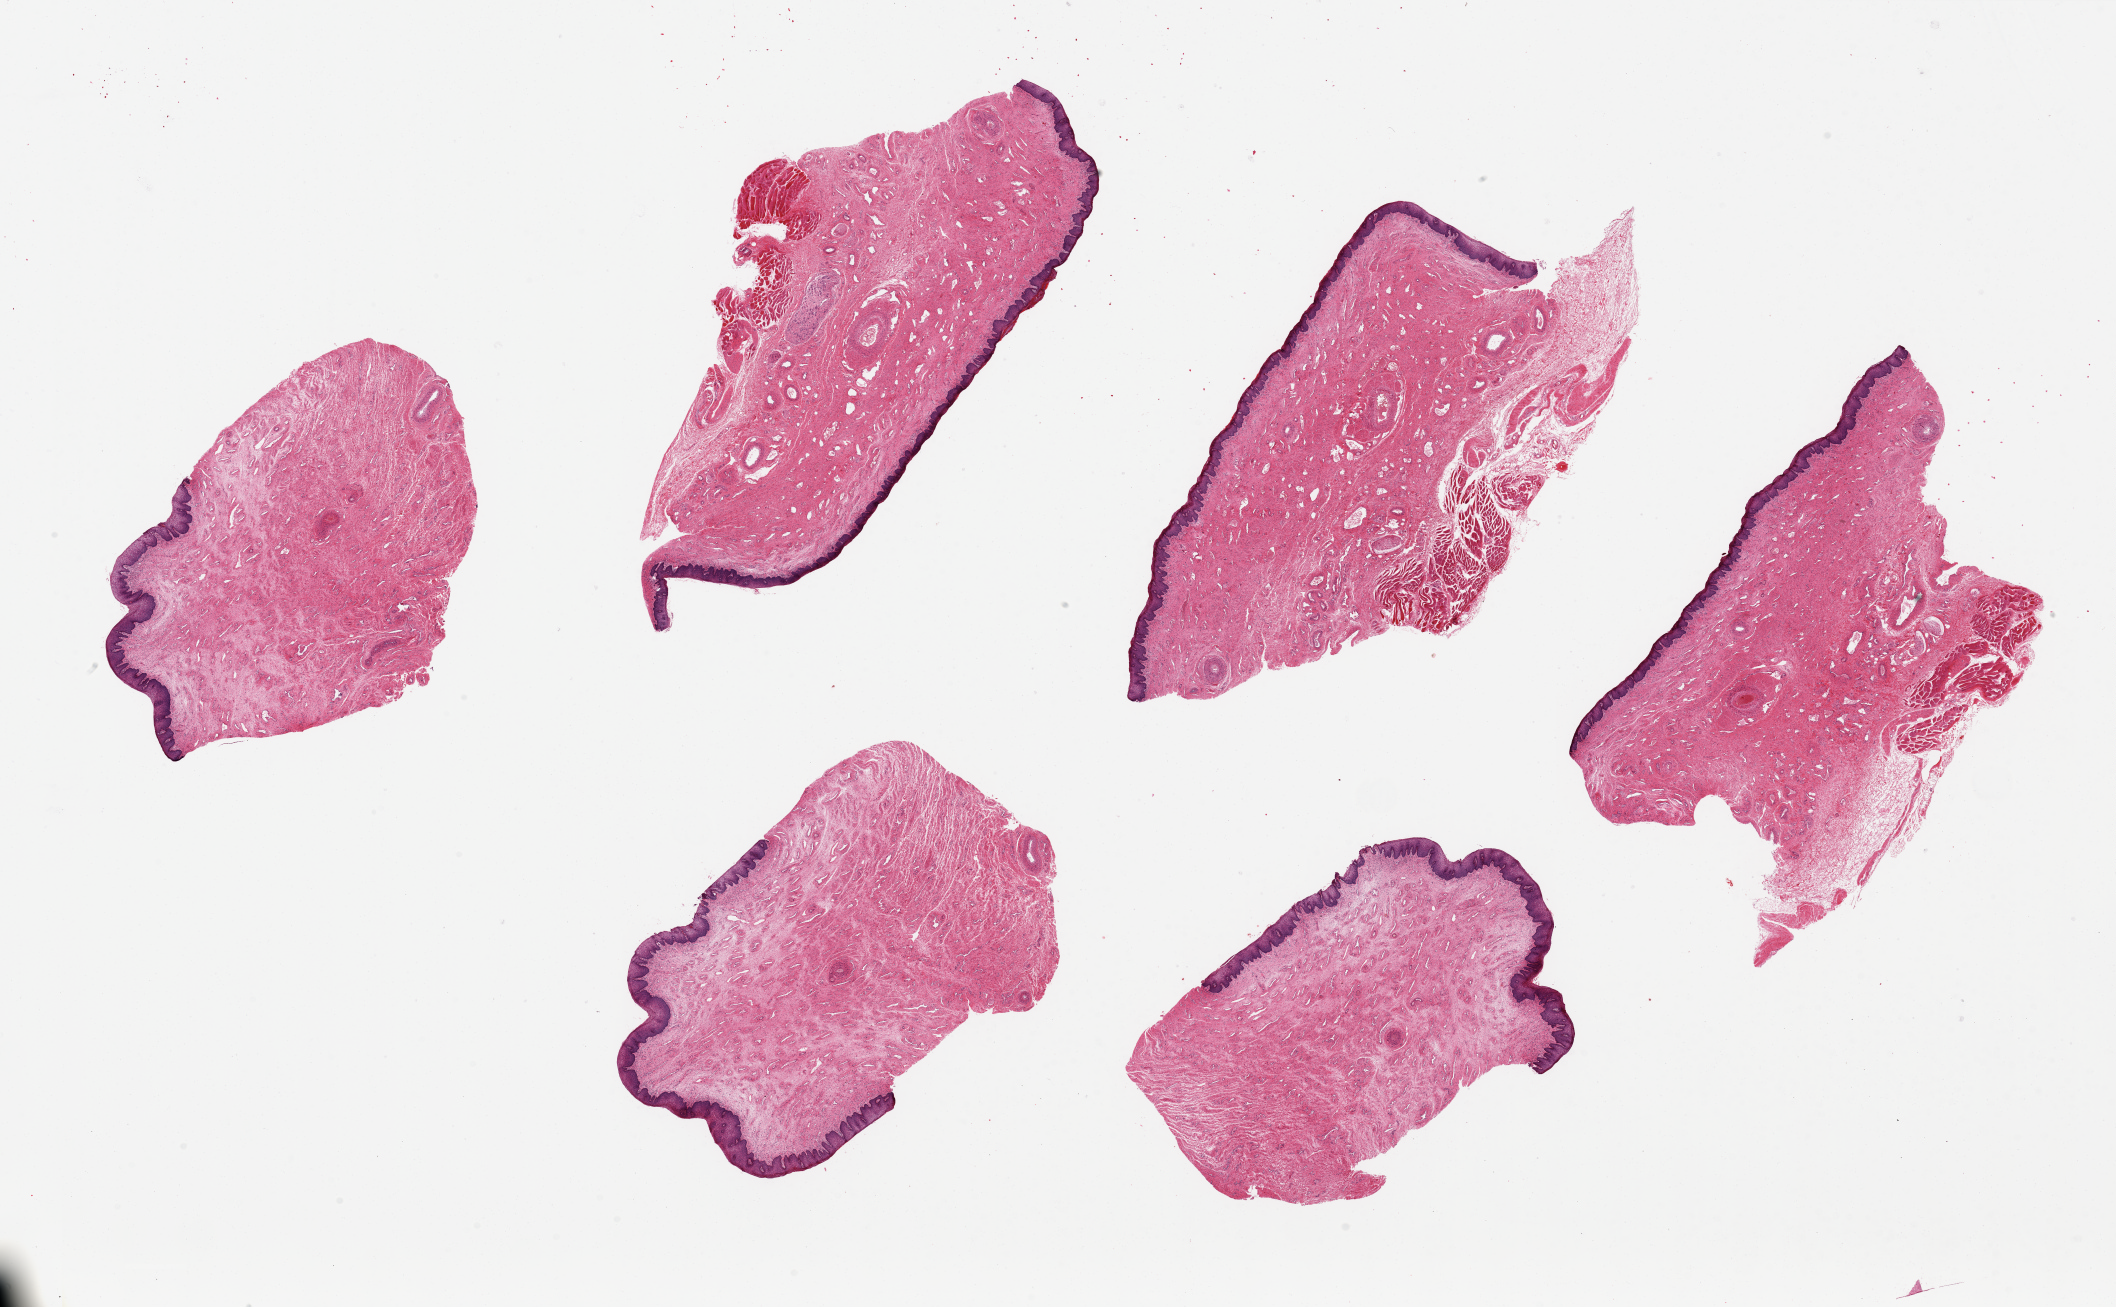
Whole-slide image, haematoxylin and eosin stain, whole scanned area (about 33.5 x 20.7 mm, from a 20x scan) shown as a low-resolution overview; PAXgene-fixed, paraffin-embedded tissue; section of vagina (target tissue); tissue donor sample. Female donor.
• pathologist's review note for this sample: 6 pieces up to 9x5 mm; excellent preservation